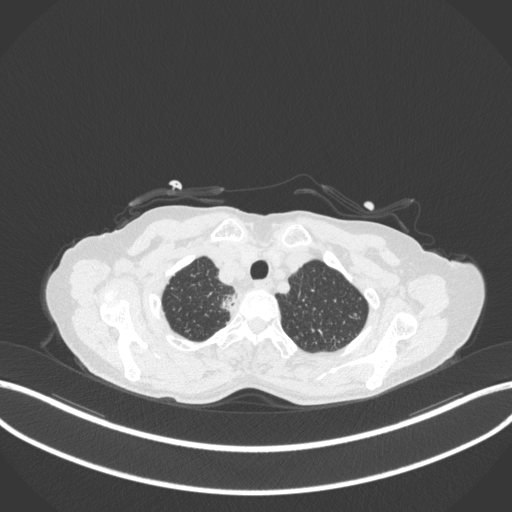
Chest CT, one axial slice. Reconstruction kernel B31f. Lung window (W 1500 / L -600 HU). 1 mm slice thickness. 512 × 512 image matrix, field of view 400 × 400 mm. Patient: female, 75 years. From the clinical record (not read from this slice): clinical TNM (as recorded): T1c N1 M1.
Annotated regions visible in this slice (bounding box drawn by a radiologist):
- lung tumour (recorded histology: adenocarcinoma): bounding box (x1, y1, x2, y2) in pixels: (216, 292, 241, 314)